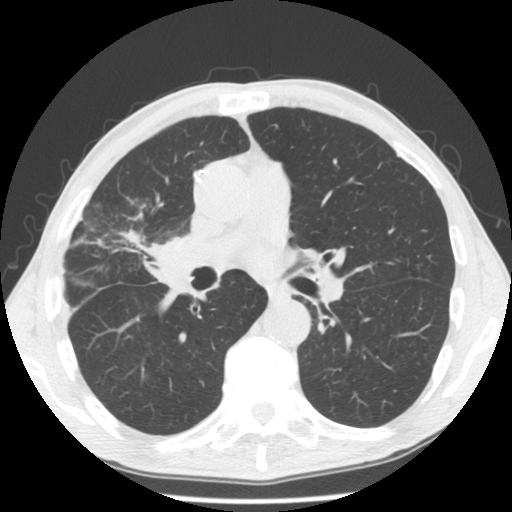
Low-dose screening chest CT, one axial slice; position 73 of 132 along the scan axis; reconstruction kernel STANDARD; lung window (W 1500 / L -600 HU); 2.5 mm slice thickness; 512 × 512 image matrix, field of view 334 × 334 mm.
Outlined on this slice (outlined manually by an expert reader):
- lesion 1 (tumor, hilum of right lung): box from (x=147, y=240) to (x=185, y=285) px